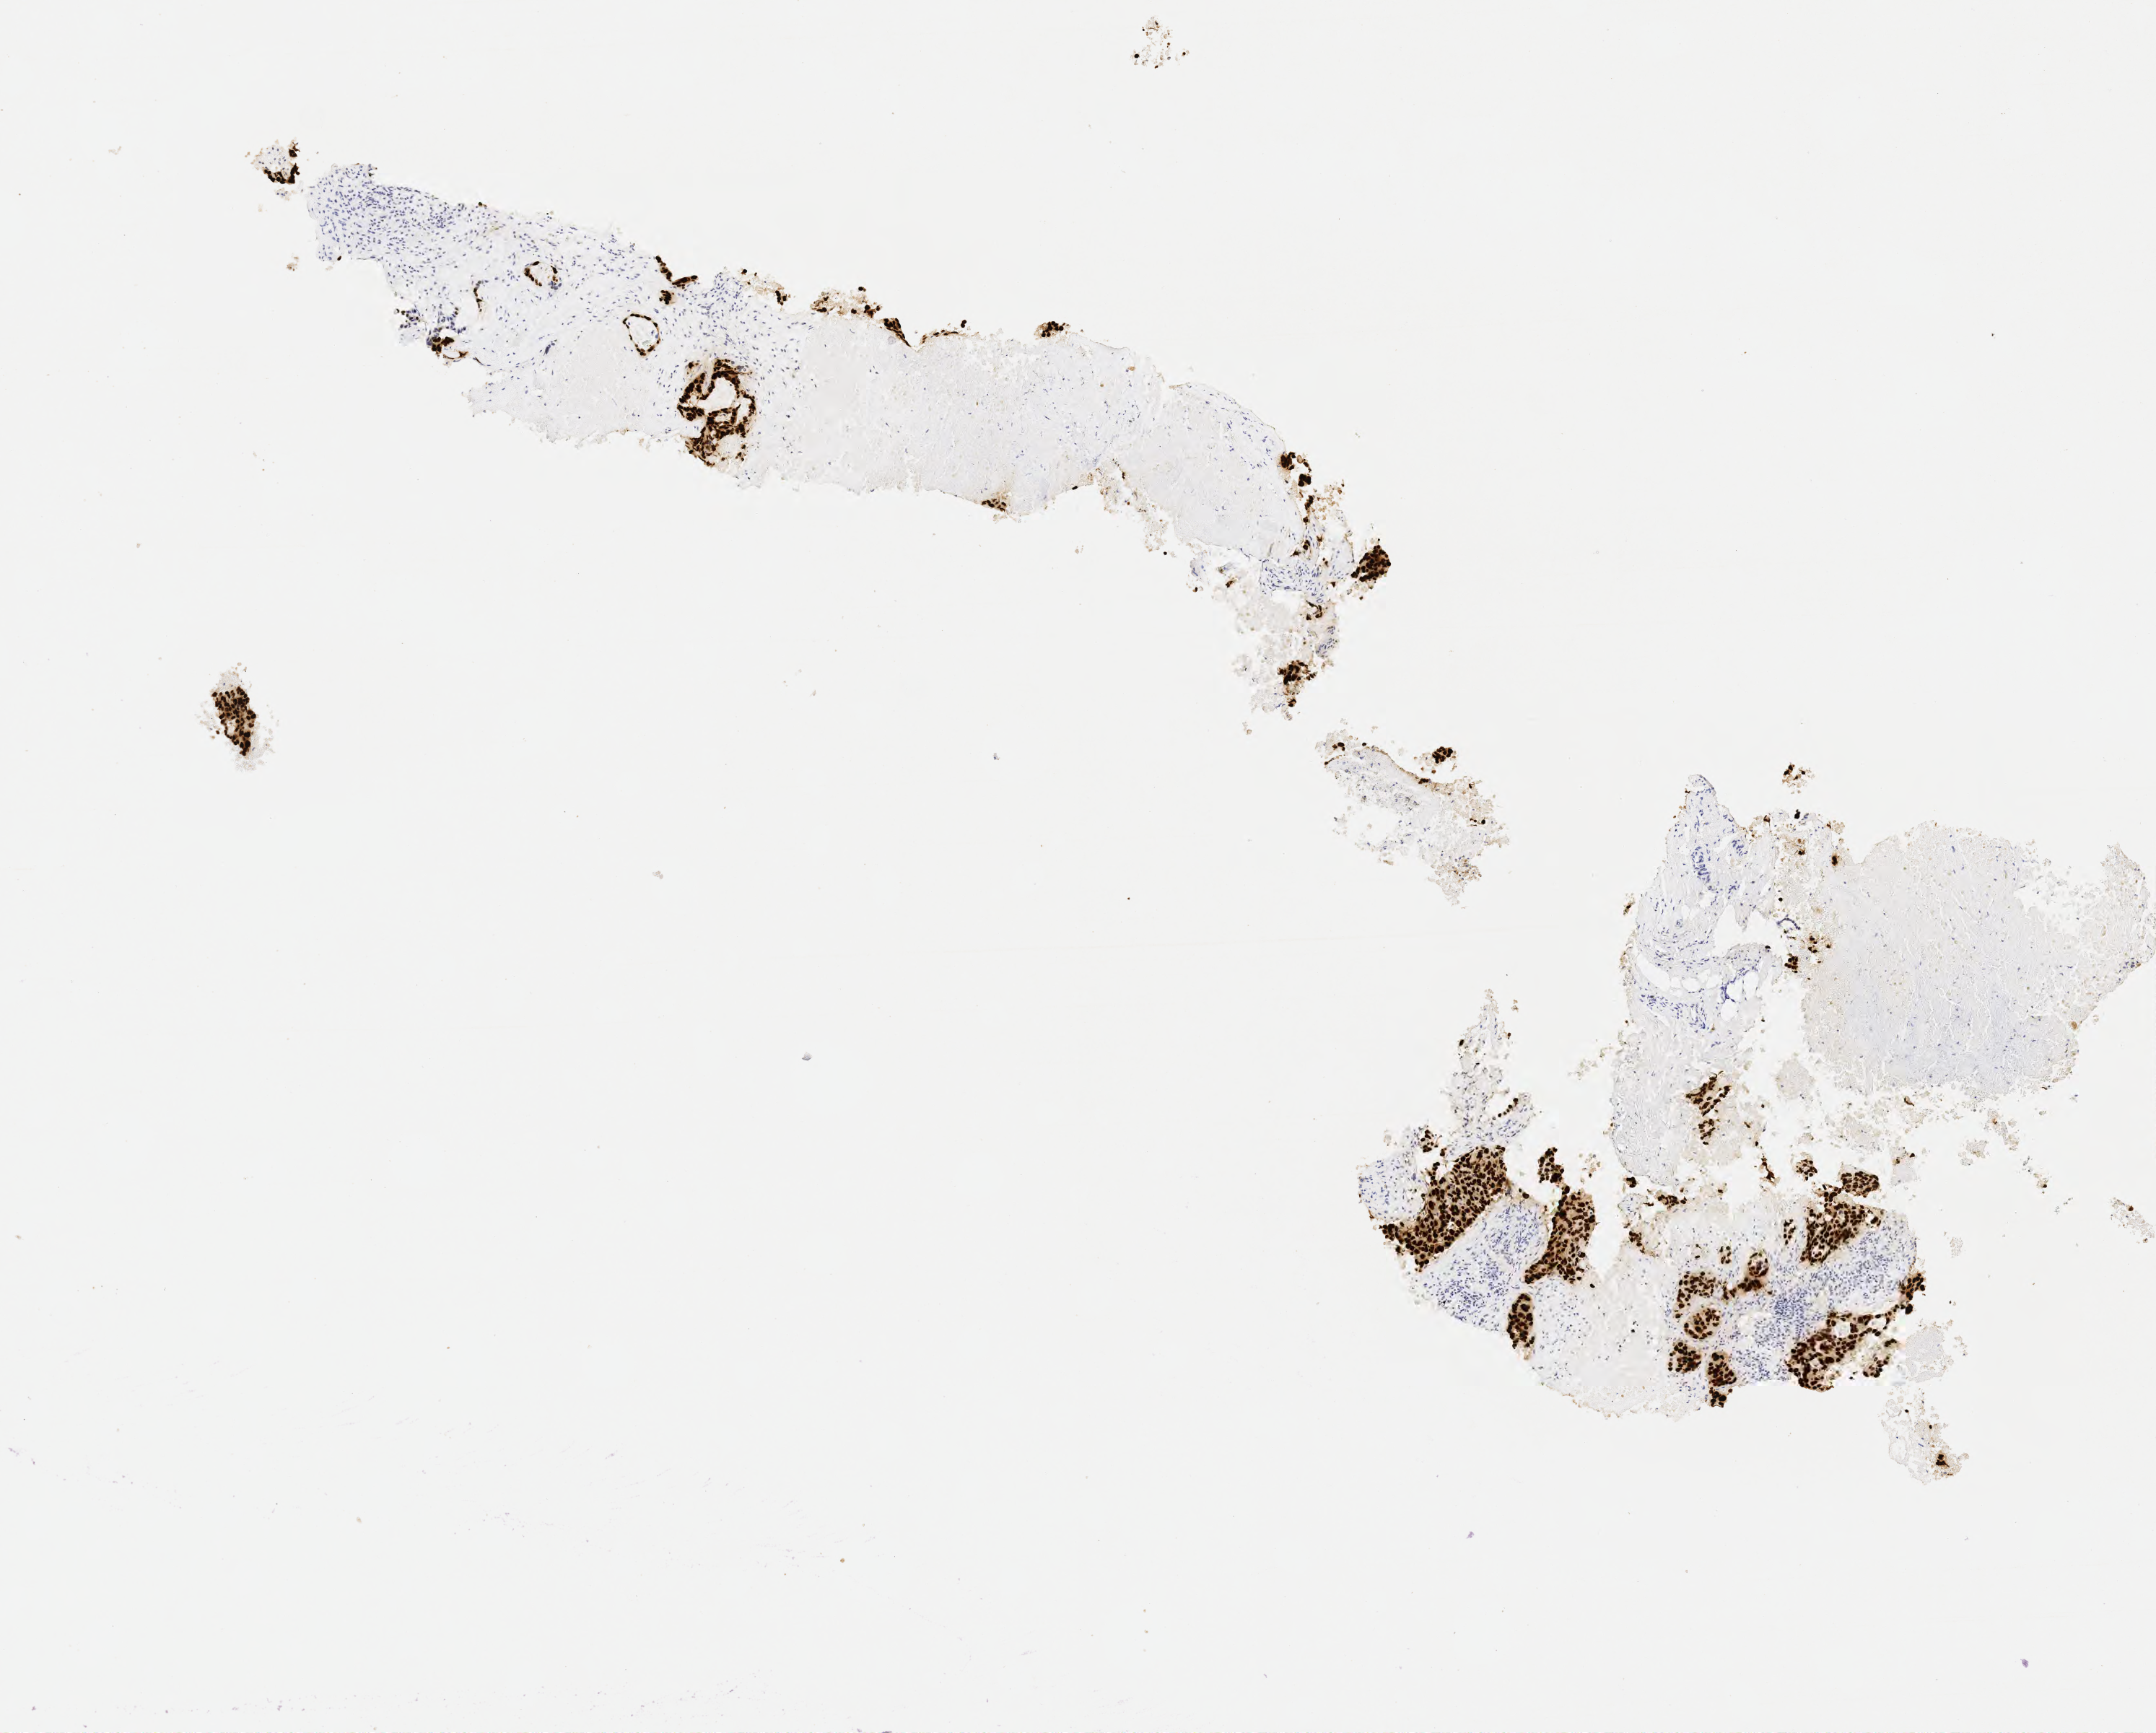
Whole-slide image, immunohistochemical stain for TTF-1 (thyroid transcription factor 1) — a low-resolution overview of the entire scanned area, about 6.0 x 4.9 mm. Specimen: tumor tissue. Site: lung (right). Patient male; age 66 years.
Histologic diagnosis: Adenocarcinoma, NOS.